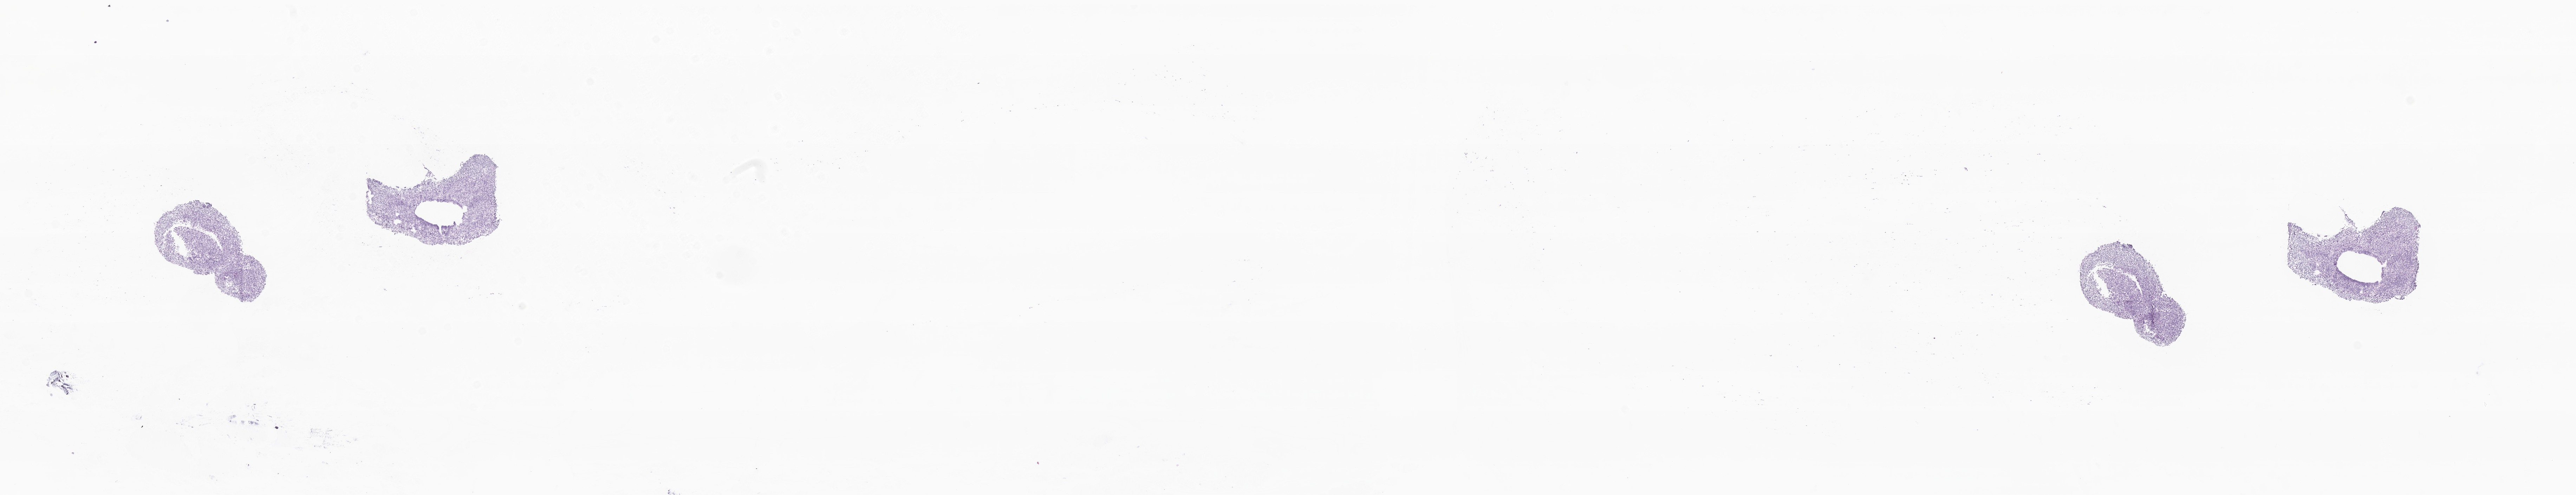
Whole-slide image, hematoxylin and eosin (H&E) stain of tumor tissue from the brain, shown as a low-resolution overview of the whole scanned area (about 30.9 x 5.9 mm). Cryosection (OCT / tissue freezing medium). Patient: male, age 61 months (5 years 1 month).
* recorded diagnosis: Medulloblastoma, NOS